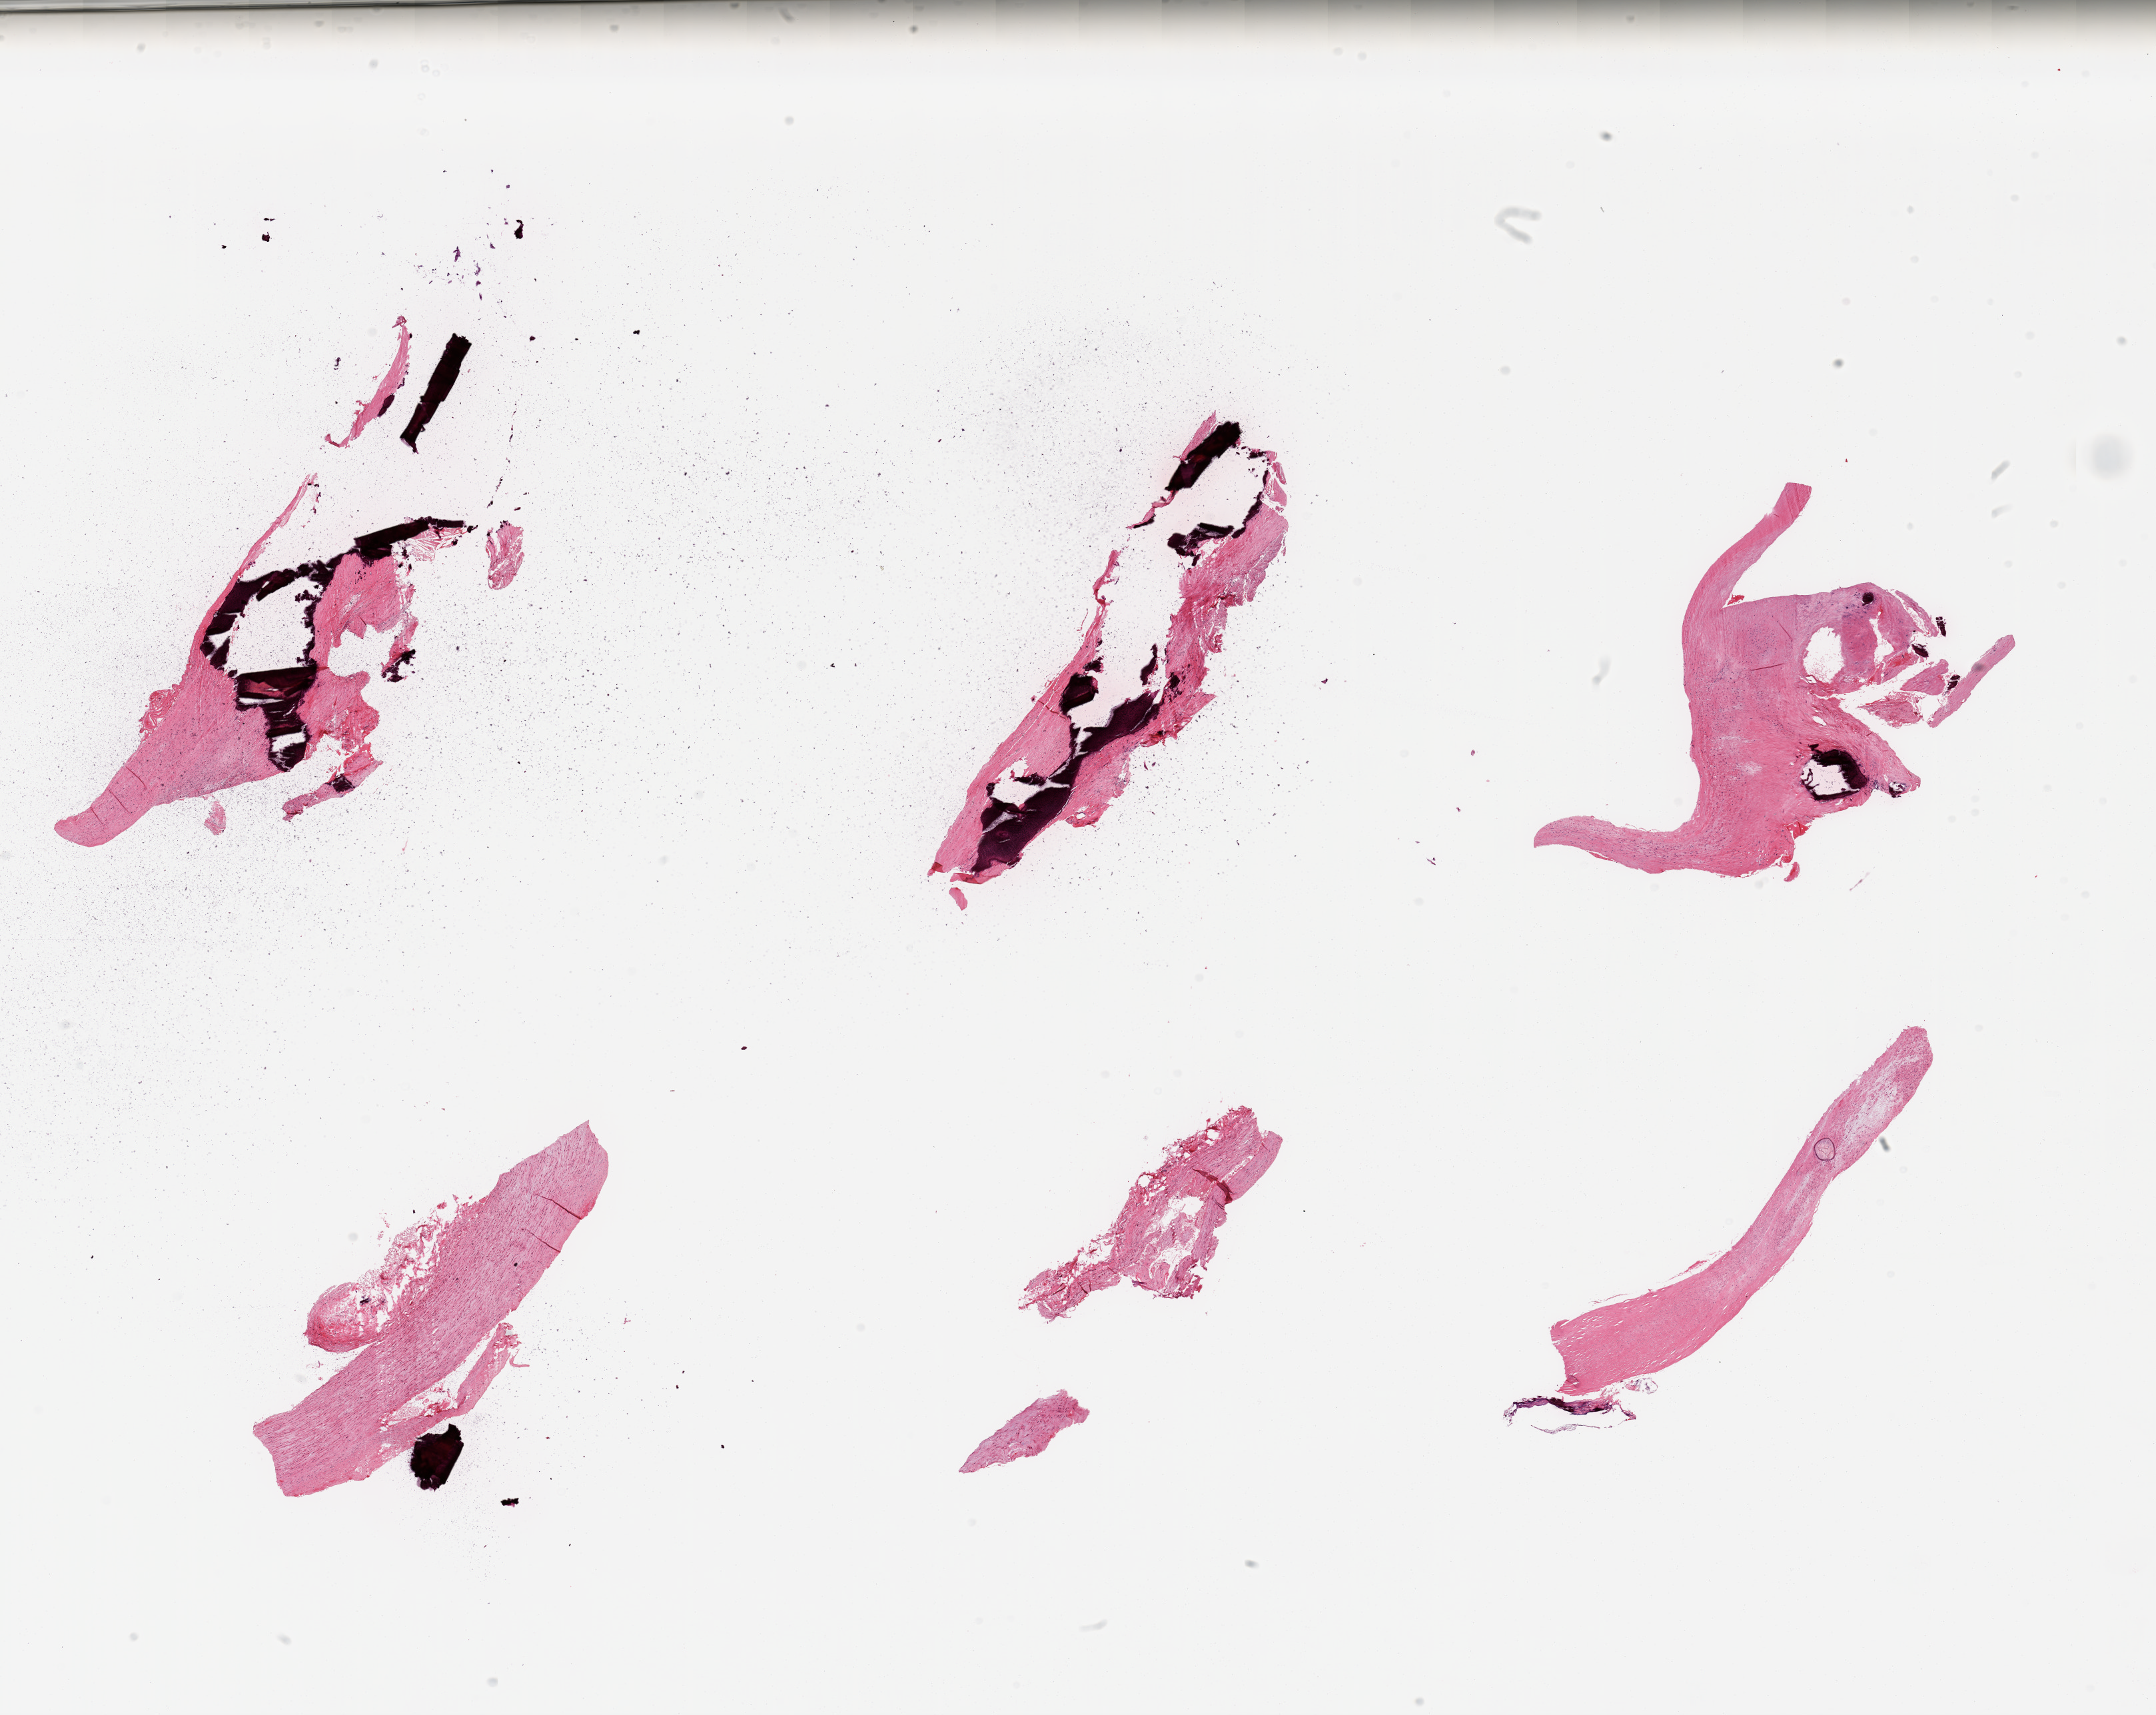
Whole-slide image, hematoxylin and eosin (H&E) stain, whole scanned area (about 25.6 x 20.4 mm) shown as a low-resolution overview; PAXgene-fixed, paraffin-embedded tissue; target tissue: aorta; tissue donor sample. Donor sex: male.
• pathologist's review note for this sample: 6 pieces, extensive calcifiedatherosis